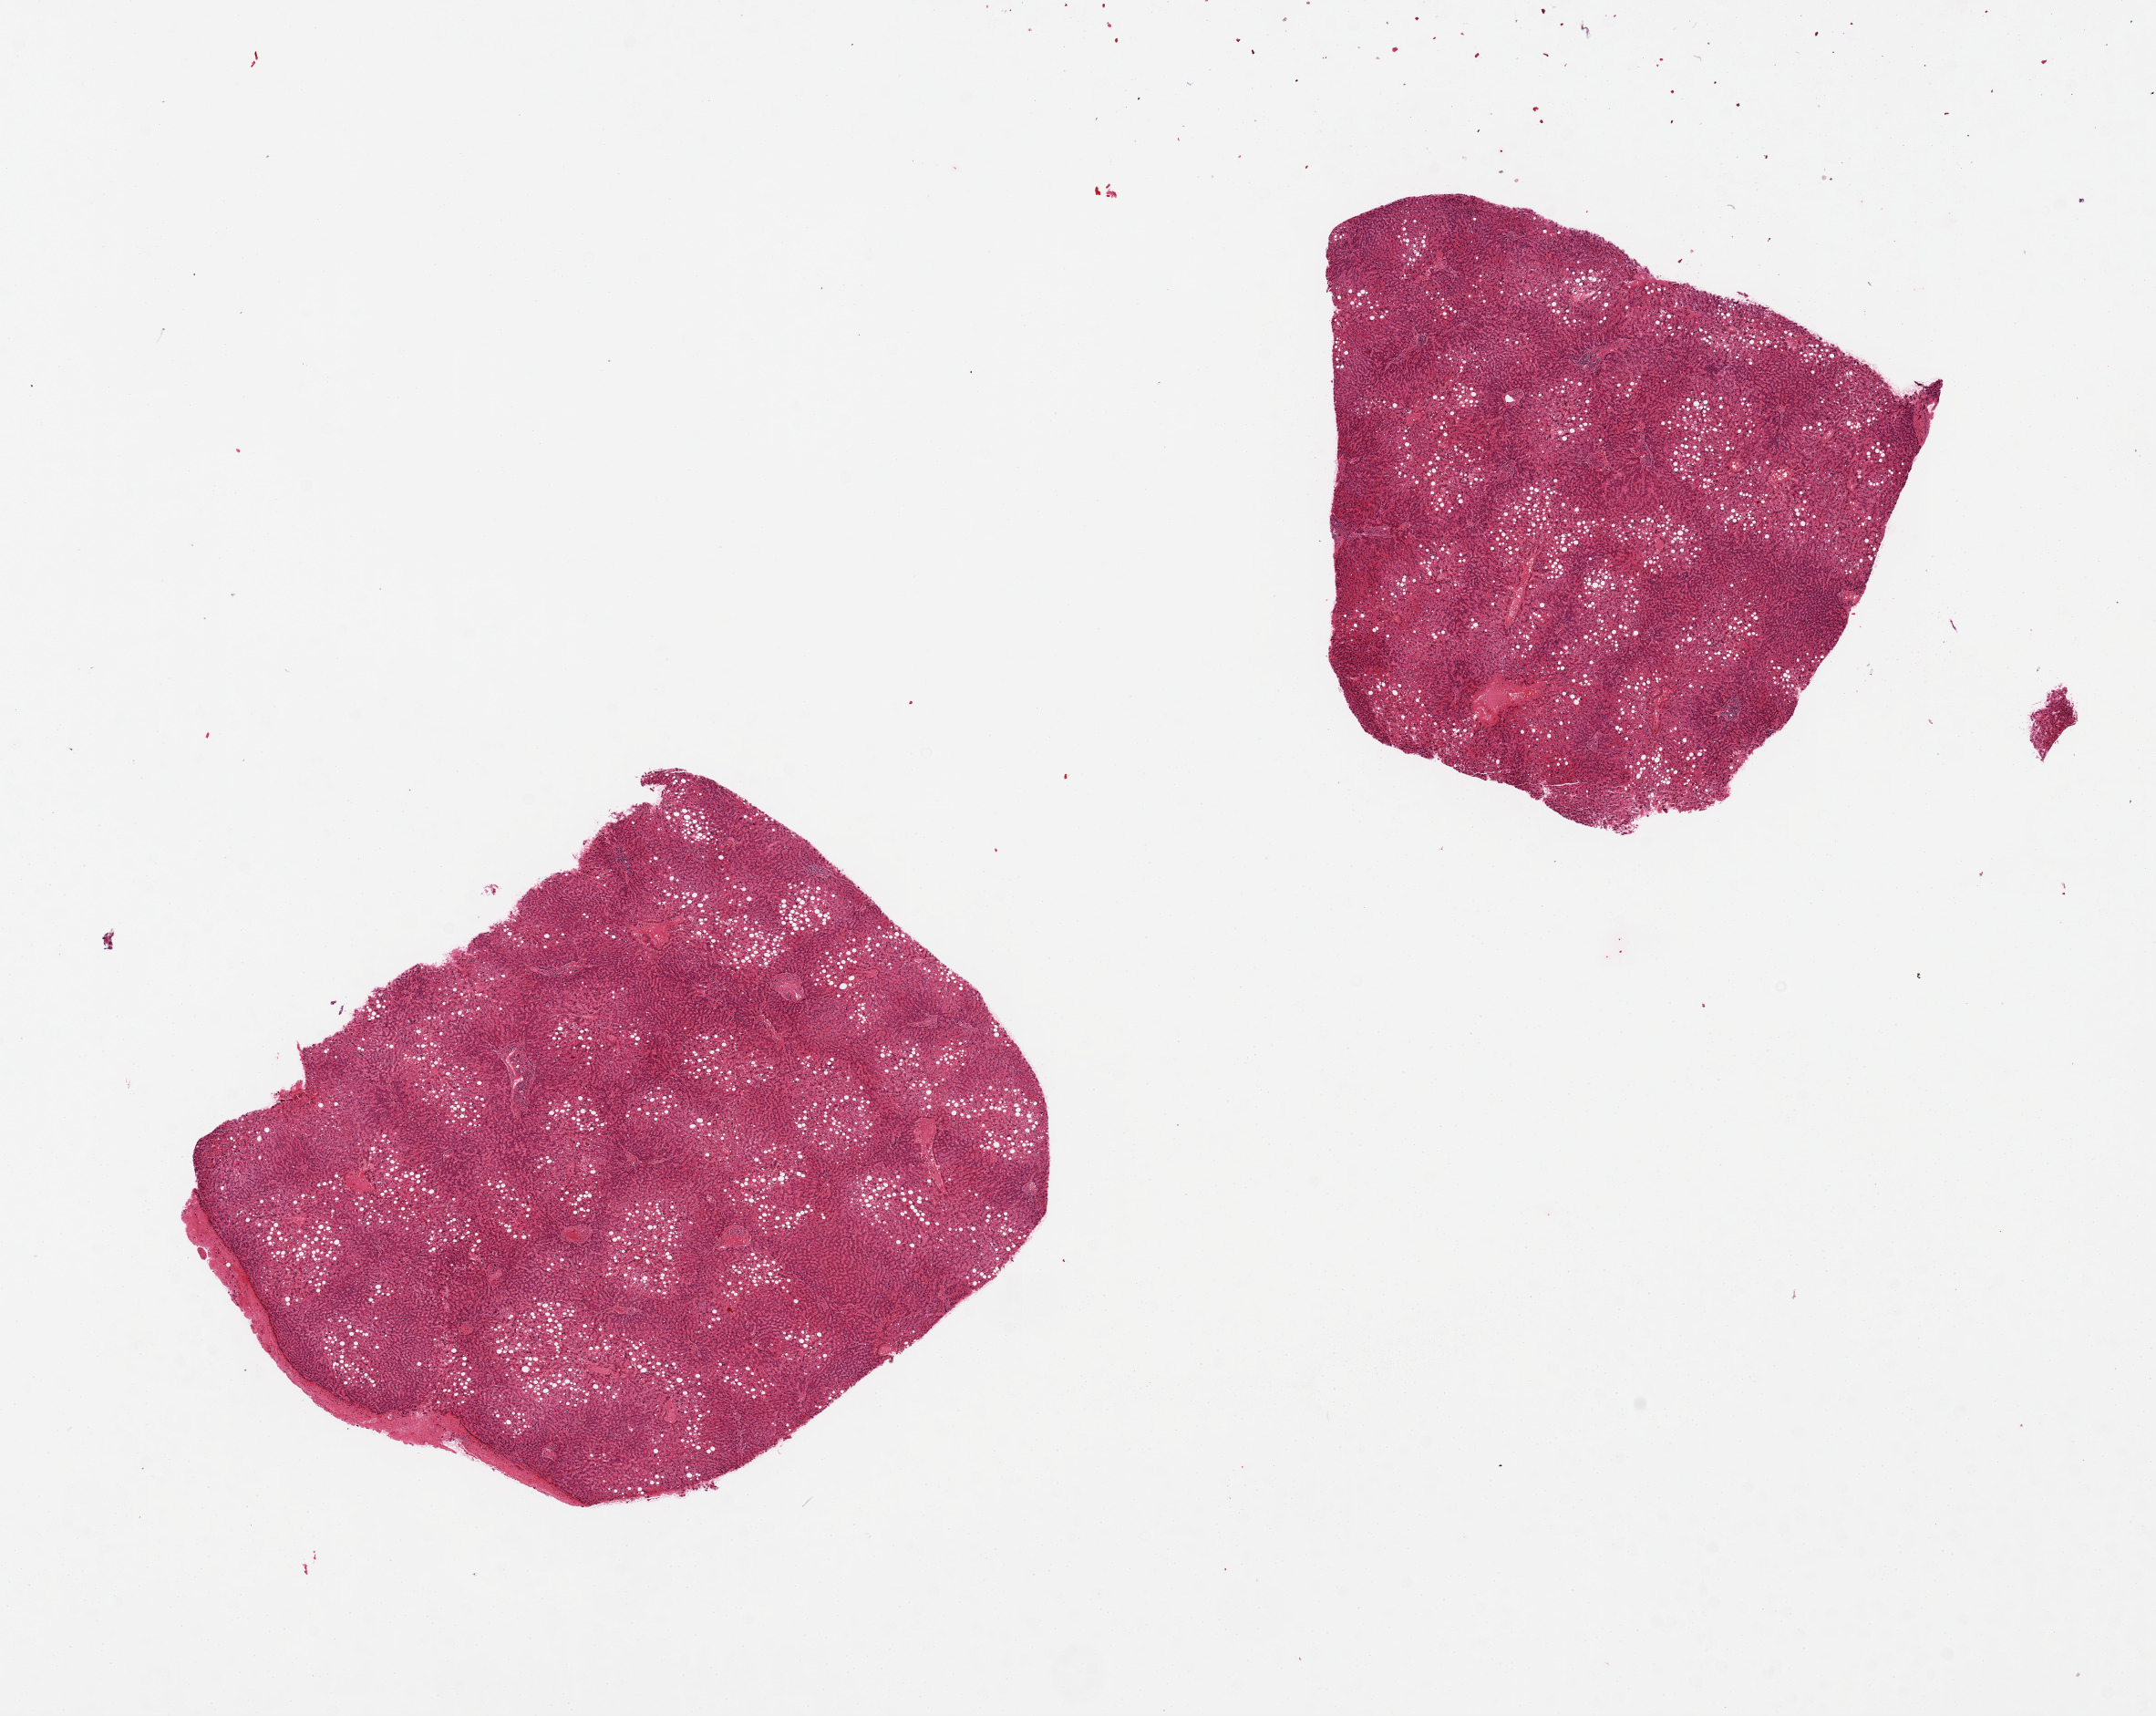
Digitized hematoxylin and eosin (H&E)-stained section, shown as a low-resolution overview of the whole scanned area (about 18.7 x 14.9 mm, slide scanned at 20x). PAXgene-fixed, paraffin-embedded tissue. Target tissue: liver. Tissue donor sample. Donor: male.
- pathologist's review note for this sample: 2 pieces, includes capsule (target is 1 cm below capsule), micro and macrovesicular steatosis